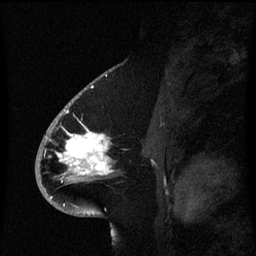
Breast MRI (dynamic contrast-enhanced), one sagittal slice; slice 37 of 60 in the series (ordered by position); dynamic contrast-enhanced series, image 2 of 3 at this slice position (ordered by acquisition); 1.5 T; TE 4.2 ms, TR 8.4 ms; 2.1 mm slice thickness; 256 × 256 image matrix. Patient: female, 53 years. From the clinical record (not read from this slice): setting: breast cancer imaged before/during neoadjuvant chemotherapy; receptor status: HR-positive, HER2-negative.
Structures marked on this image (semi-automatic segmentation, software-assisted and operator-edited):
- analysis volume of interest (the breast-tissue region the enhancement analysis was run in; not a lesion): box from (x=49, y=108) to (x=119, y=201) px
- tumour enhancement mask (voxels above the 70 % enhancement threshold inside the analysis volume of interest): (x=52, y=126)–(x=113, y=199)